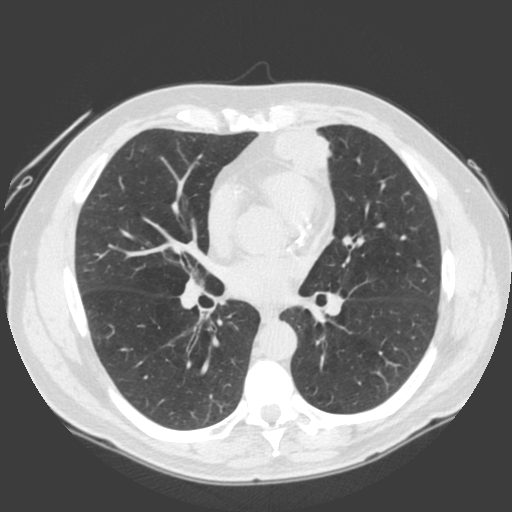
Low-dose screening chest CT, one axial slice; position 94 of 185 along the scan axis; 120 kVp; lung window (W 1500 / L -600 HU); 512 × 512 image matrix, field of view 360 × 360 mm.
Annotated regions visible in this slice (manually delineated by an expert):
- lesion 1 (tumor, lower lobe of left lung): bounding box (x1, y1, x2, y2) in pixels: (275, 124, 332, 176)